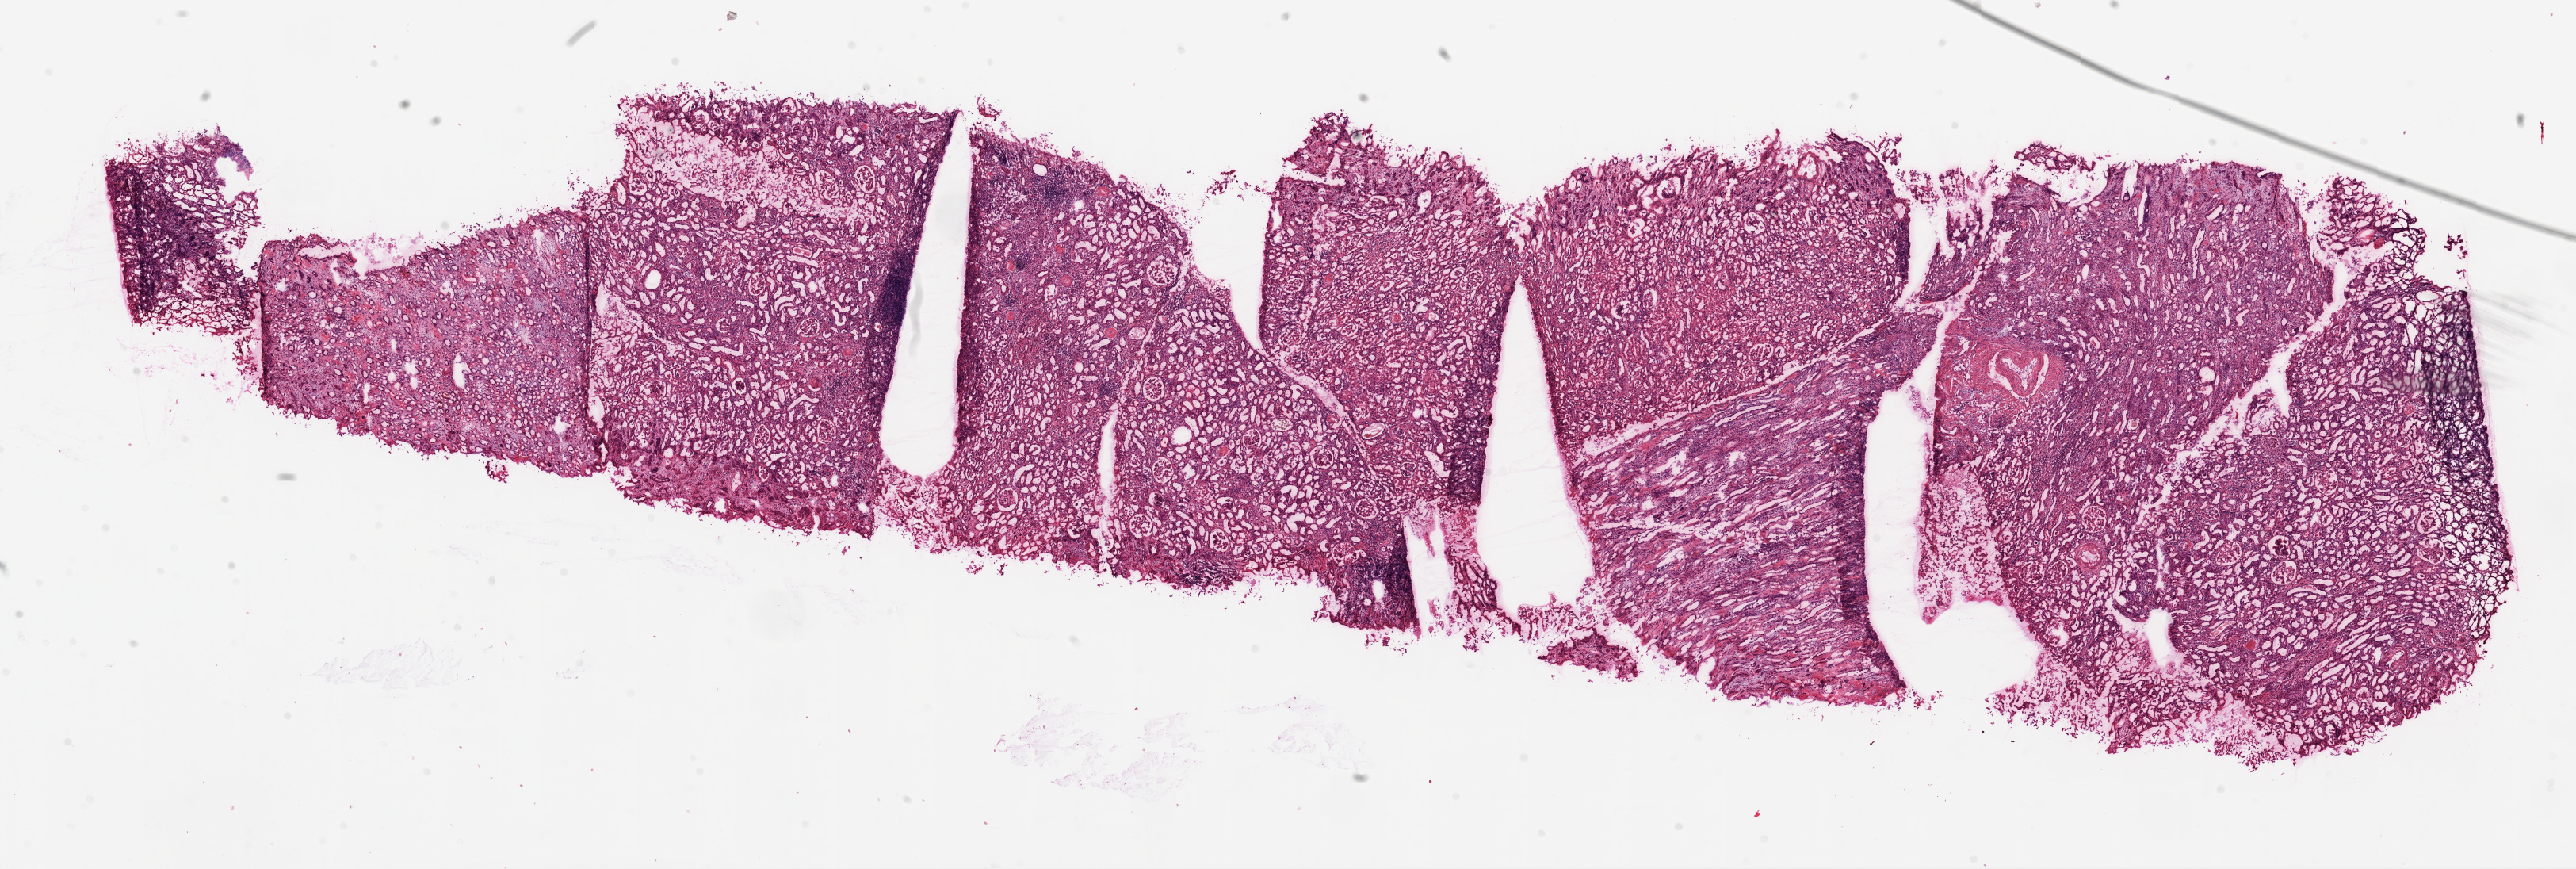
Digitized Hematoxylin and eosin (H&E) stained tissue section (whole slide) — a low-resolution overview of the entire scanned area, about 26.1 x 8.8 mm (from a 20x scan), frozen section, sample: solid tissue normal (non-tumour tissue), kidney. Male patient; age at initial diagnosis 72 years.
* this section: solid tissue normal (non-tumour) sample from the same patient
* patient diagnosis: Clear cell adenocarcinoma, NOS